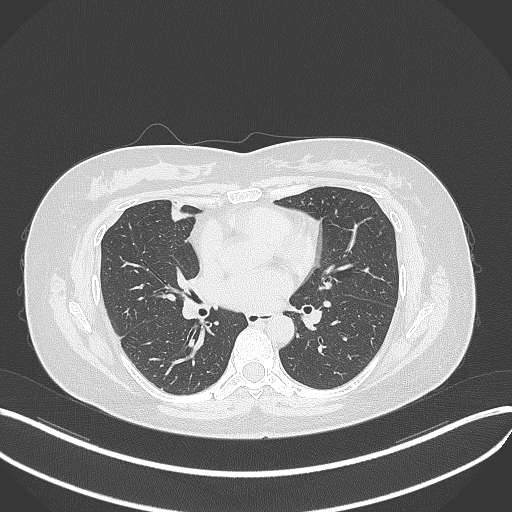
Chest CT, one axial slice; slice 156 of 273 in the series (ordered by position); reconstruction kernel B70f; 120 kVp; lung window (W 1500 / L -600 HU); 1 mm slice thickness; 512 × 512 image matrix, field of view 400 × 400 mm. Female patient, age 42 years. From the clinical record (not read from this slice): clinical TNM (as recorded): T1b N0 M0.
Annotated regions visible in this slice (bounding box drawn by a radiologist):
- lung tumour (recorded histology: adenocarcinoma): box from (x=165, y=199) to (x=201, y=228) px